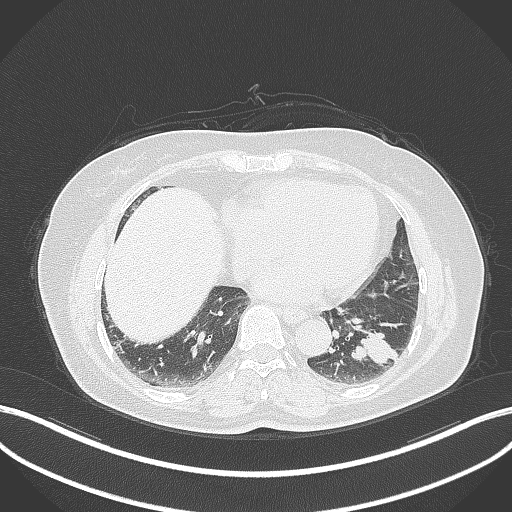
Chest CT, one axial slice; slice 129 of 311 in the series (ordered by position); 120 kVp; lung window (W 1500 / L -600 HU); 512 × 512 image matrix, field of view 400 × 400 mm. Patient: female, 59 years. Case-level facts recorded for this patient, not image findings: clinical TNM (as recorded): T2a N0 M0.
Annotated regions visible in this slice (bounding box drawn by a radiologist):
- lung tumour (recorded histology: adenocarcinoma): box from (x=346, y=324) to (x=398, y=364) px